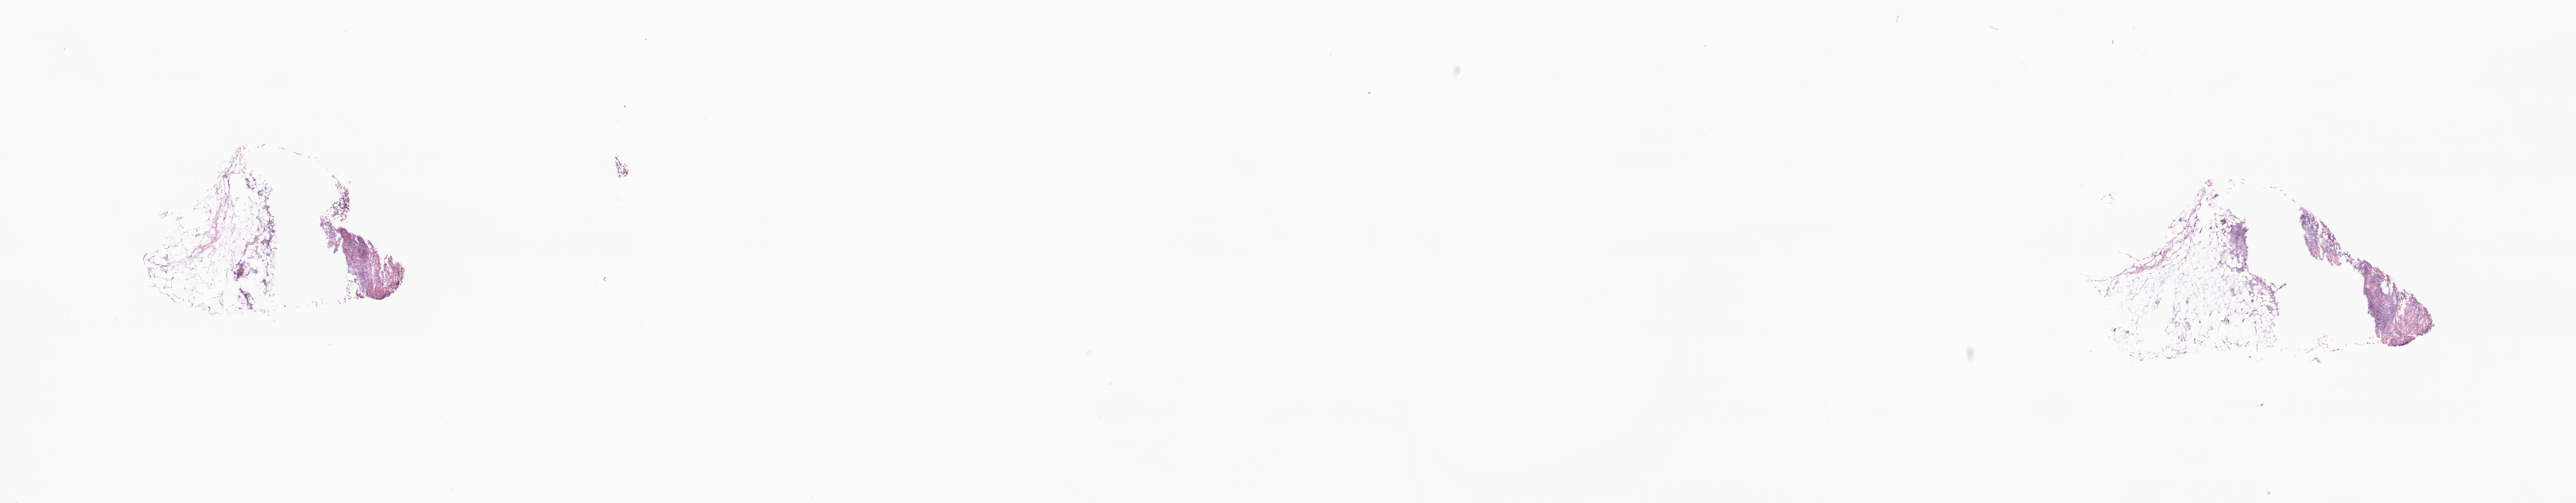
Haematoxylin and eosin whole-slide image, a low-resolution overview of the entire scanned area, about 33.4 x 6.5 mm, frozen section, primary tumor, site: breast. Female, age 58 years at initial diagnosis.
Diagnosis: Infiltrating duct carcinoma, NOS.